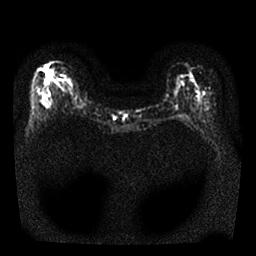
Breast MRI, one axial slice; diffusion-weighted series; image 2 of 4 stored at this slice position (different b-values; order by instance number); 1.5 T; 256 × 256 image matrix, field of view 300 × 300 mm. Female patient.
Outlined on this slice (manually delineated by an expert):
- tumour on diffusion-weighted imaging: box from (x=45, y=71) to (x=51, y=82) px